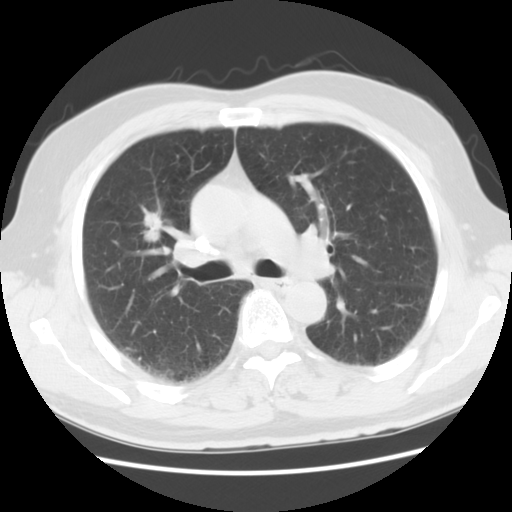
Low-dose screening chest CT, axial slice. Second screening round (one year after baseline). Lung window (W 1500 / L -600 HU). 5 mm slice thickness. Standard (soft-tissue) reconstruction kernel (STANDARD). Slice 28 of 70 in the series. 512 × 512 image matrix. Male, age 59 years at enrolment.
- Lesion marked by an expert reader, bounding box (x1, y1, x2, y2) in pixels: (131, 205, 170, 250).
- The exam's reader record, not a measurement of the box and not confirmed to be the same lesion: non-calcified nodule or mass ≥4 mm, right upper lobe, 20 × 13 mm, spiculated (stellate) margins, soft tissue attenuation, pre-existing on the prior screen: yes; interval growth: yes.
- Official screen result: positive, other.
- Later outcome: lung cancer diagnosed 267 days after this screen — large cell carcinoma, NOS, right upper lobe, poorly differentiated (G3), stage IIIA (AJCC 6th edition), 34 mm at pathology.